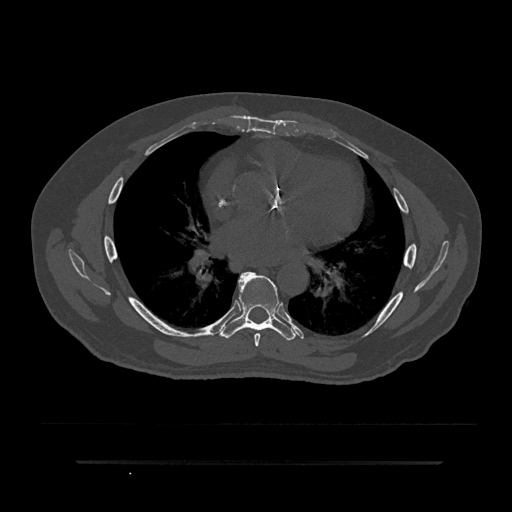
CT including the spine, one axial slice; position 493 of 797 along the scan axis; reconstruction kernel Br40s/3; bone window (W 1800 / L 400 HU); 512 × 512 image matrix. Patient: male, 59 years. From the clinical record (not read from this slice): primary cancer: bile ducts; vertebrae with lytic lesions (as recorded): T10.
Annotated regions visible in this slice (semi-automatically segmented with operator editing):
- T6 vertebra: bounding box (x1, y1, x2, y2) in pixels: (239, 276, 261, 347)
- T7 vertebra: (220, 272, 296, 341)